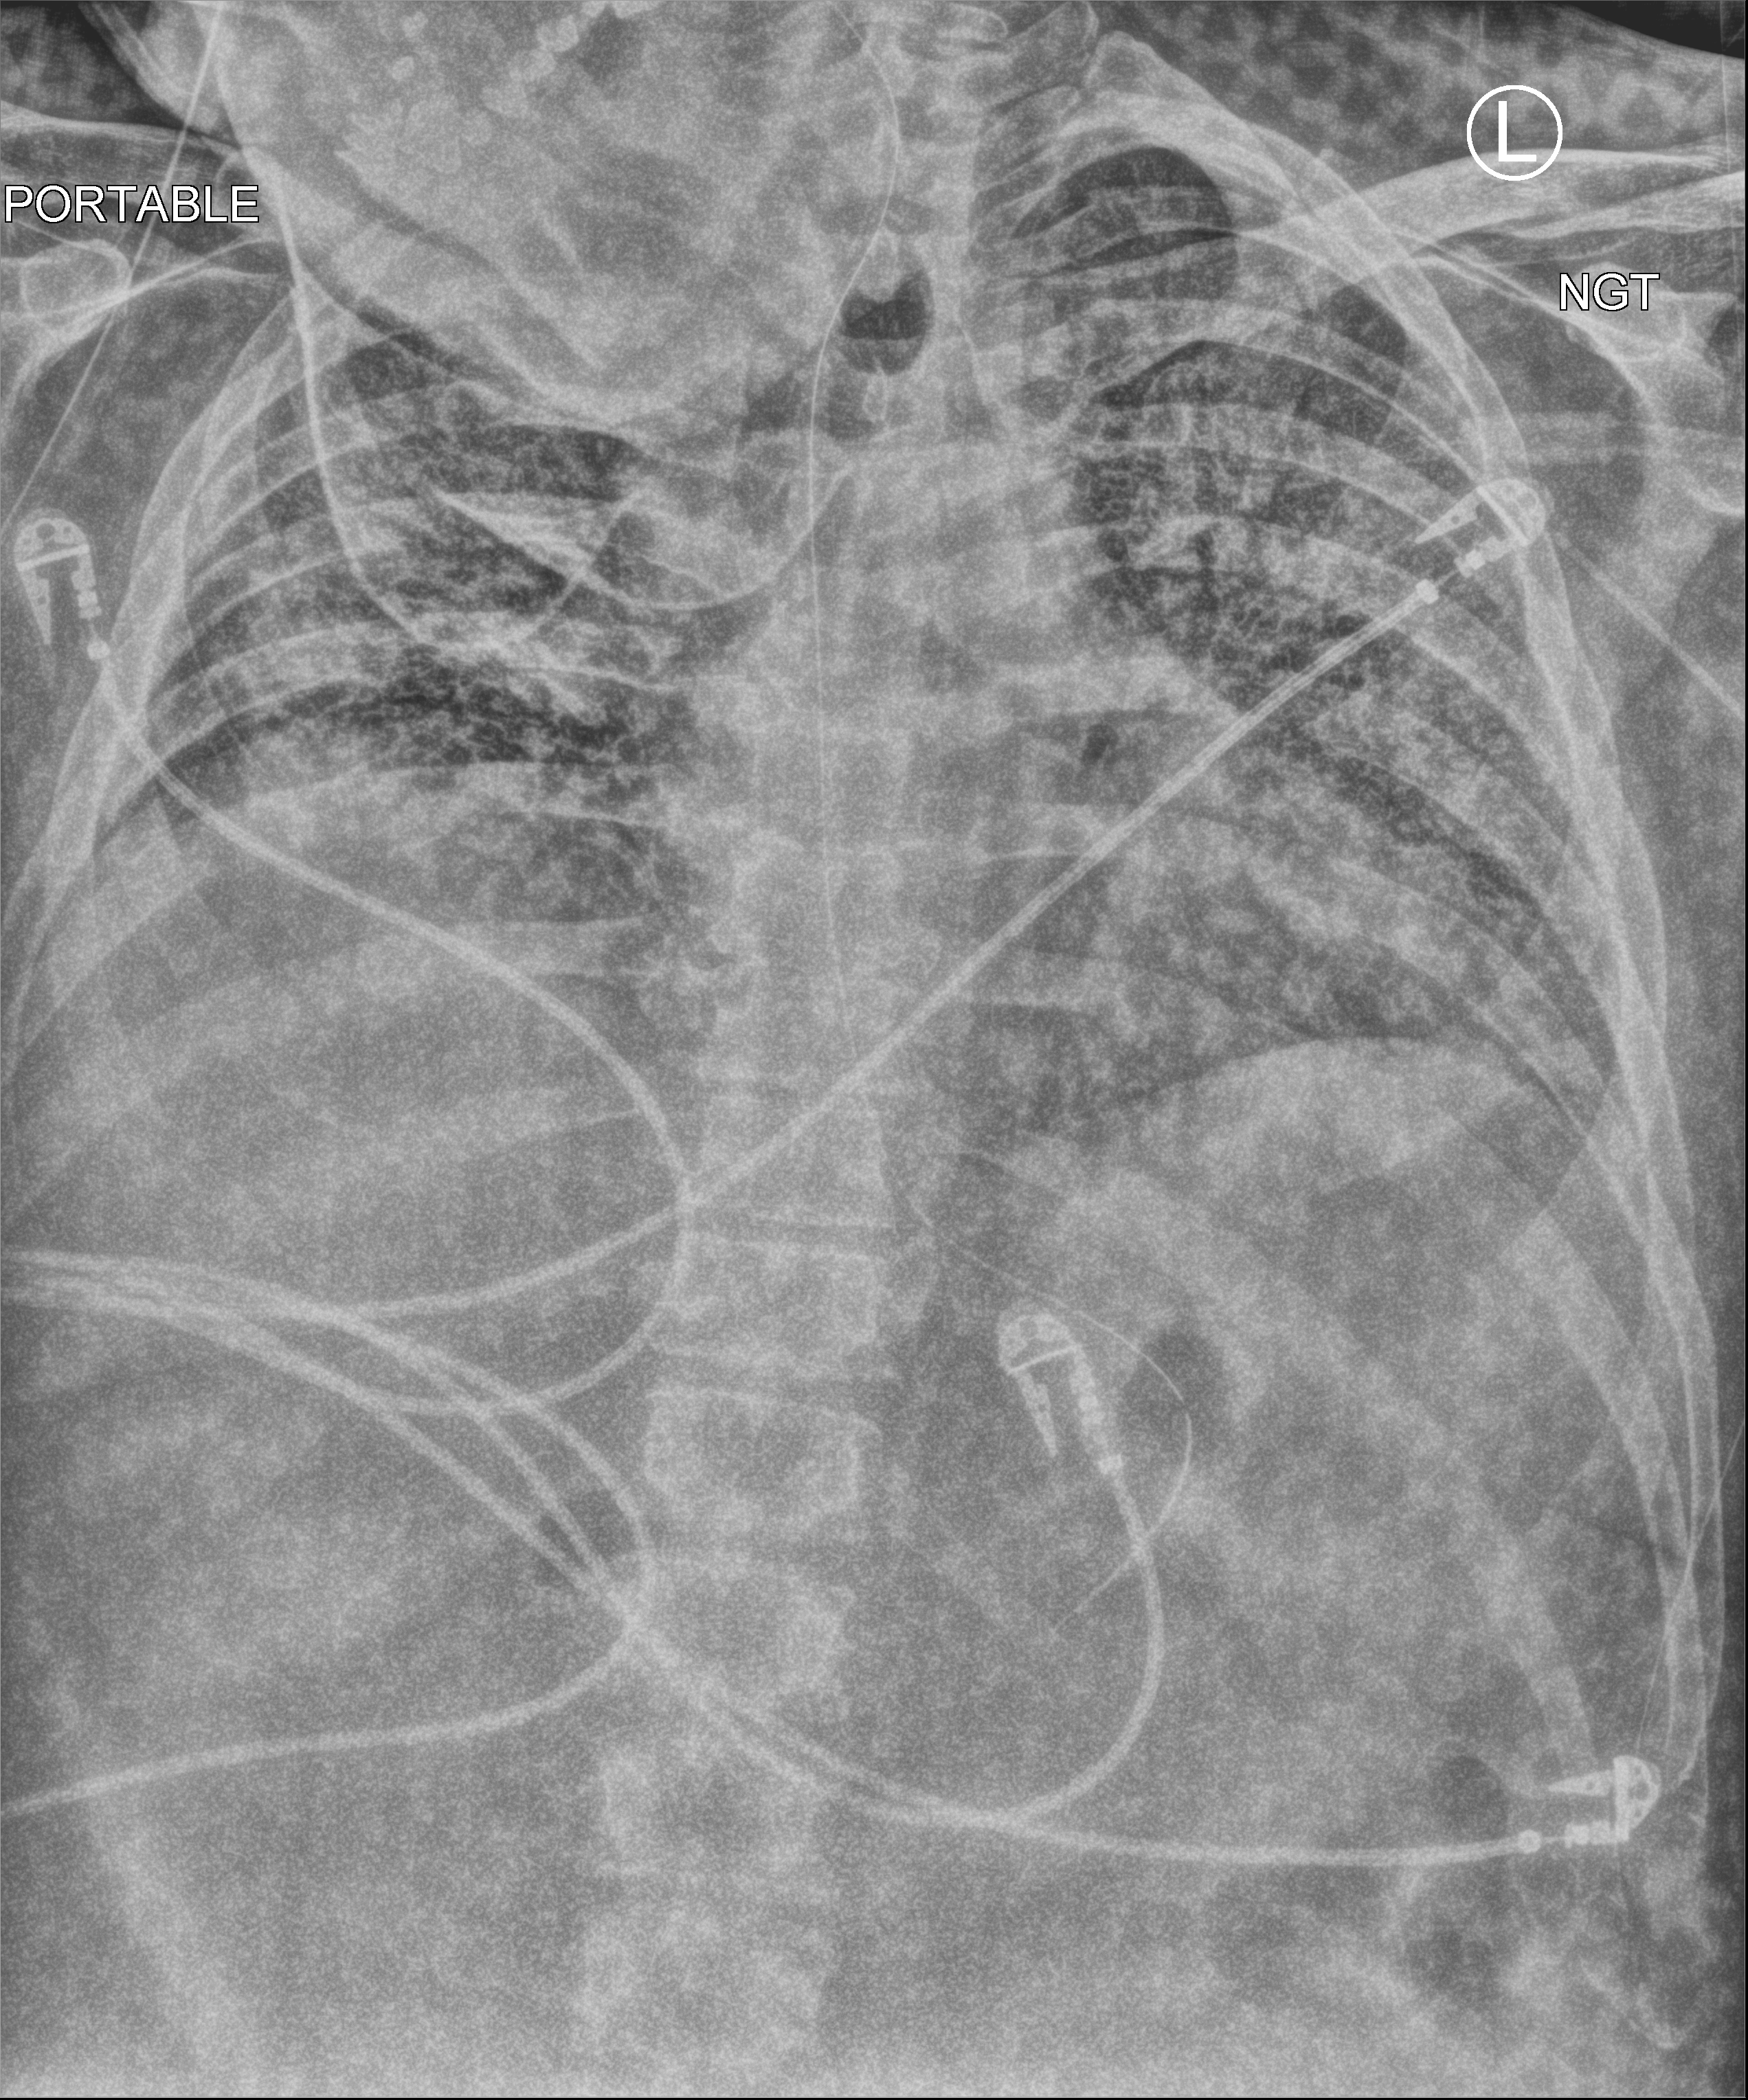
Bedside chest radiograph (computed radiography); anteroposterior (AP) projection. Patient hospitalised with COVID-19; male, aged 18–59 years.
Hospital-stay facts (about this admission, not read from this image; timing relative to this image not recorded):
- hypertension (admission record): yes
- admitted to intensive care during this hospital stay: yes